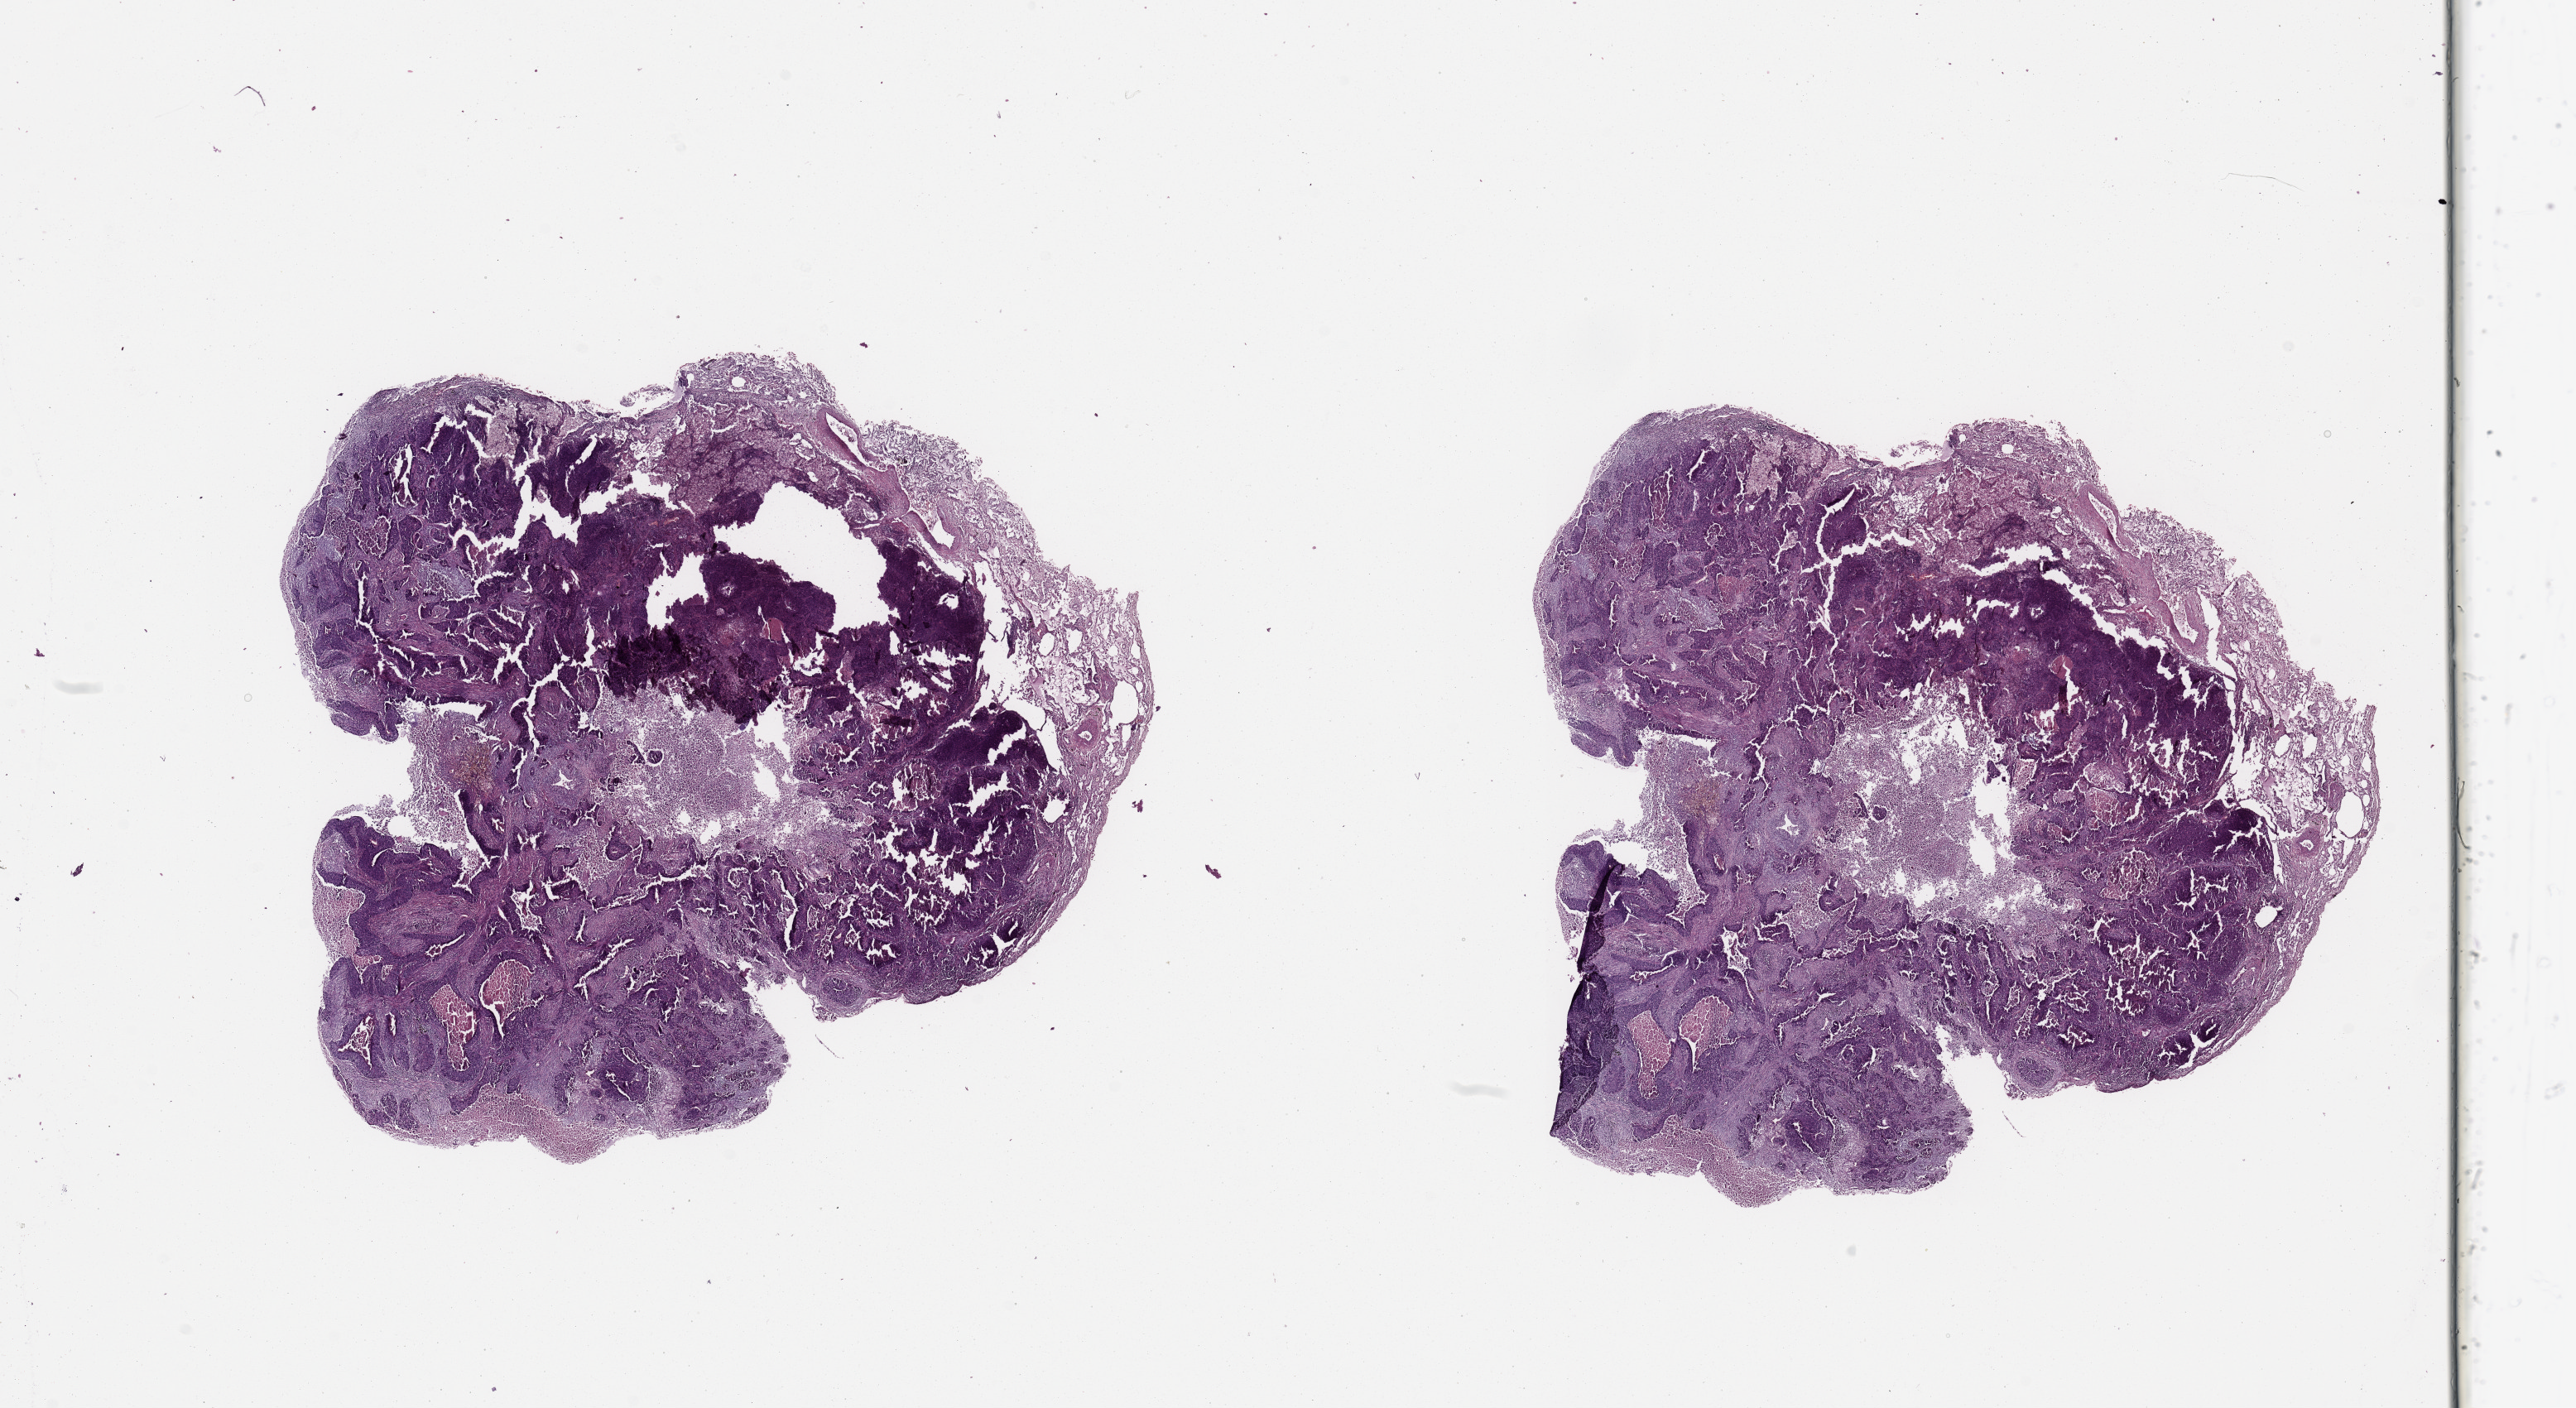
Digitized H&E-stained tissue section (whole slide) — a low-resolution overview of the entire scanned area, about 24.6 x 13.5 mm (from a 20x scan). Lung, tumour tissue. Male, 76 y/o. Histologic grade: G2 (moderately differentiated).
• histologic diagnosis: Squamous cell carcinoma, NOS
• primary tumour site (as recorded): right middle lobe
• AJCC pathologic stage: IA